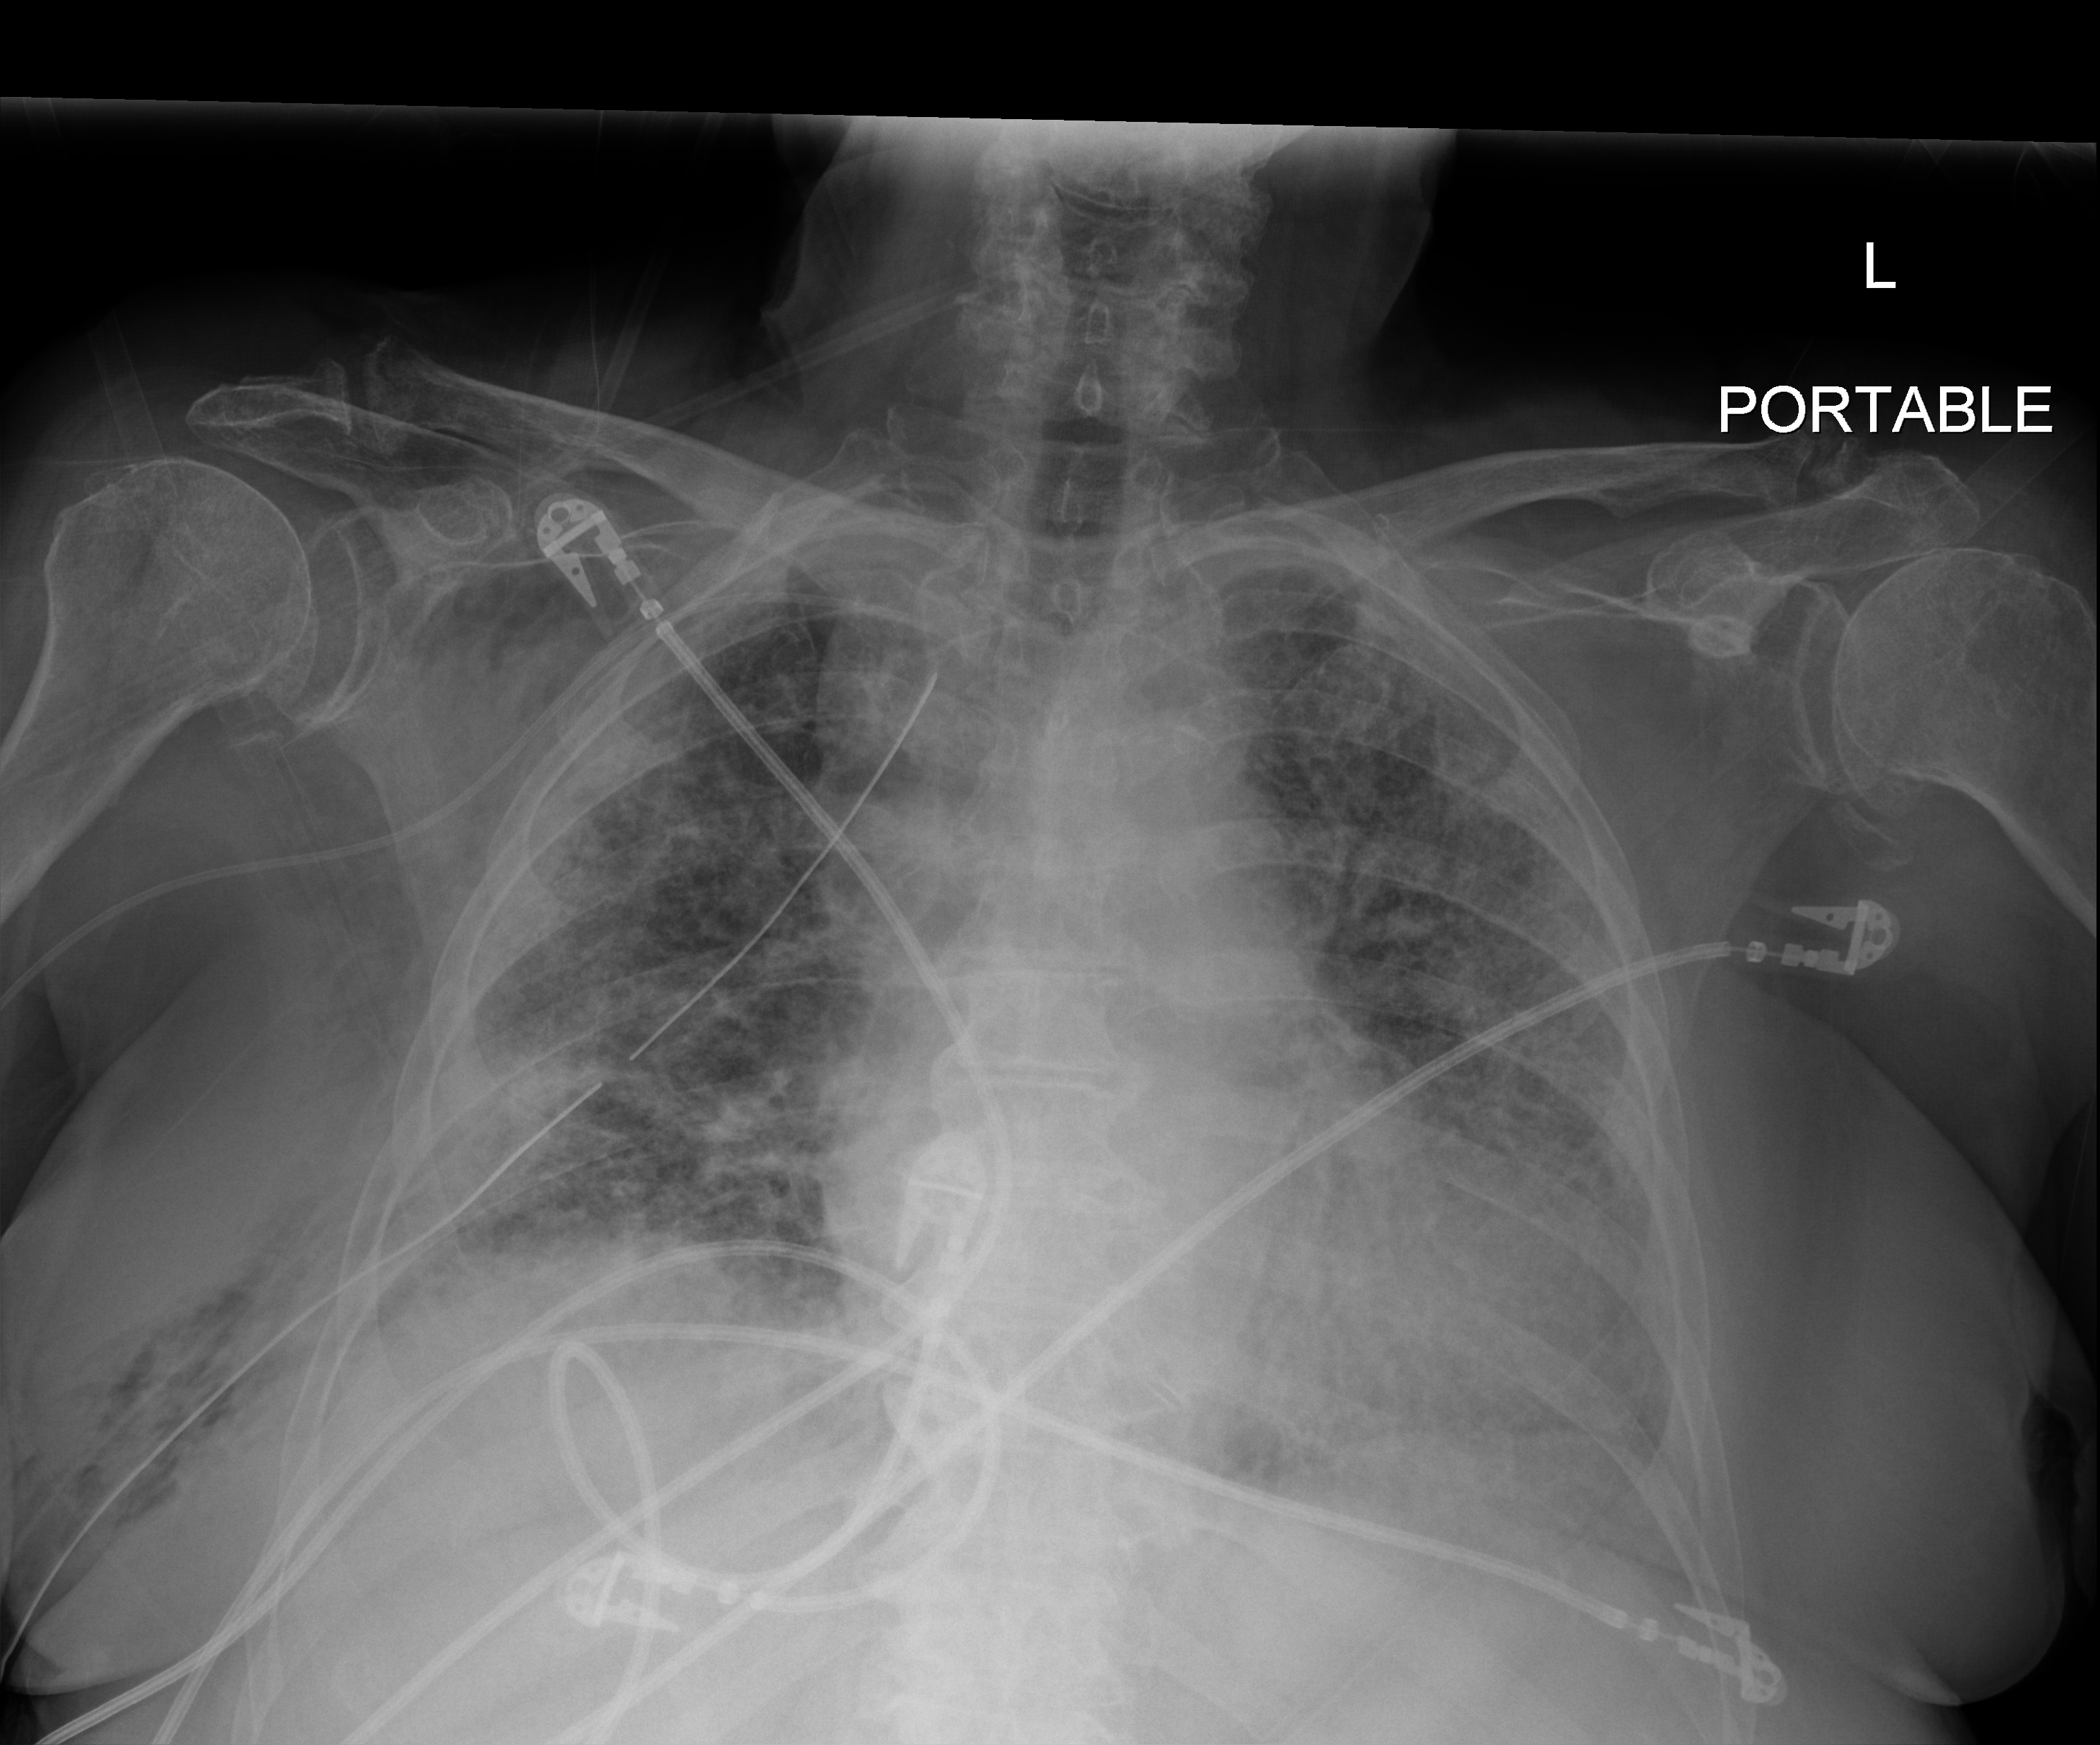
Portable chest radiograph, anteroposterior (AP) projection. Patient hospitalised with COVID-19; female, aged 75–90 years.
From the hospital-stay record, not from the radiograph (when in the stay this image was taken is not recorded): mechanically ventilated during this hospital stay: yes; COPD (admission record): no.